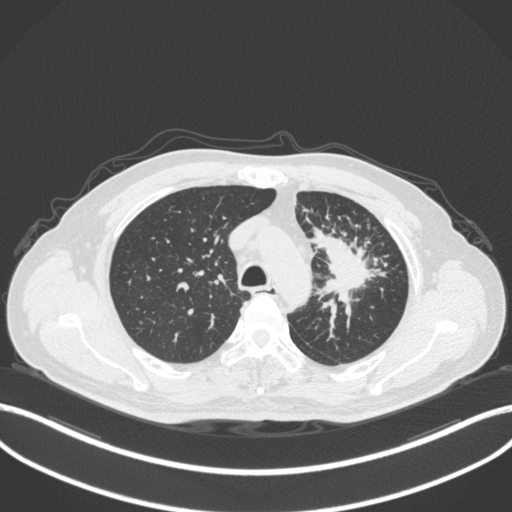
Chest CT, one axial slice; position 267 of 386 along the scan axis; lung window (W 1500 / L -600 HU); 512 × 512 image matrix, field of view 400 × 400 mm. Male patient, age 69 years. From the clinical record (not read from this slice): clinical TNM (as recorded): T2a N2 M0.
Annotated regions visible in this slice (bounding box drawn by a radiologist):
- lung tumour (recorded histology: adenocarcinoma): box from (x=313, y=225) to (x=380, y=319) px